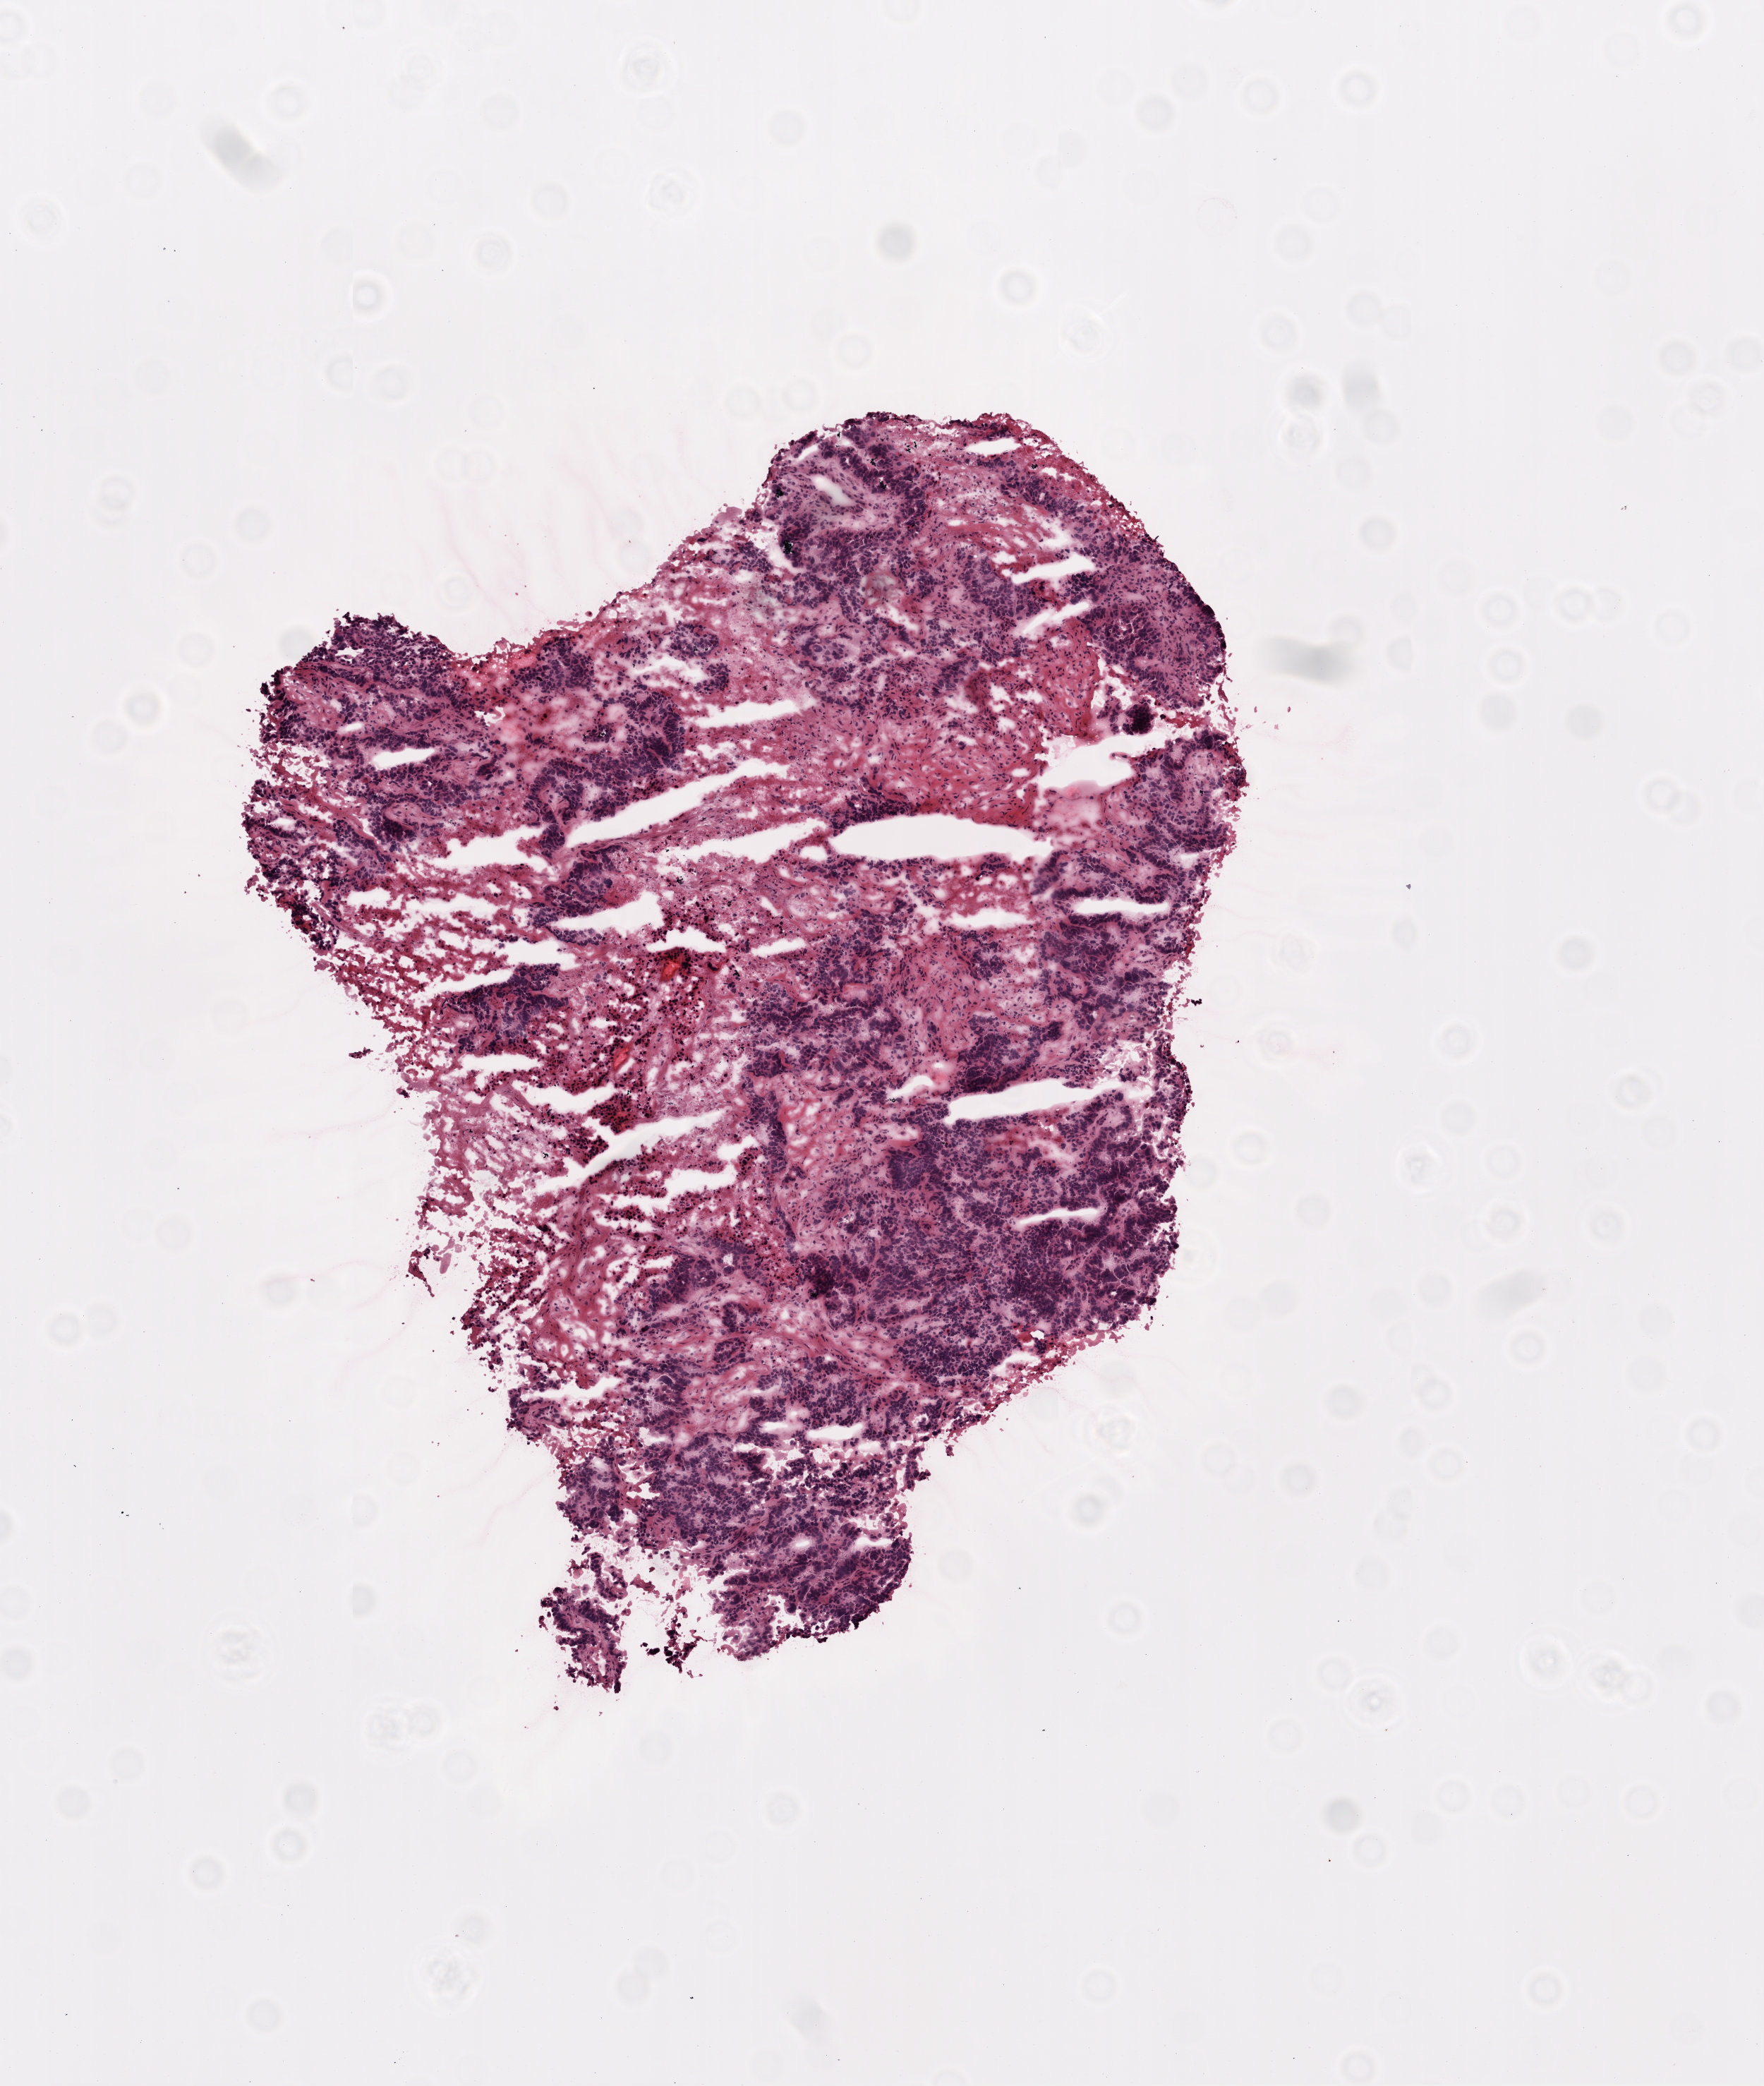
Whole-slide histology image, H&E — low-resolution overview of the scanned area, about 5.0 x 5.9 mm; frozen section; recurrent tumour sample from the ovary. Patient: female, age at initial diagnosis 54 years. Slide review estimates, as recorded: tumour cells 50%, tumour nuclei 90%.
This section: recurrent tumour. Patient diagnosis: Serous cystadenocarcinoma, NOS.